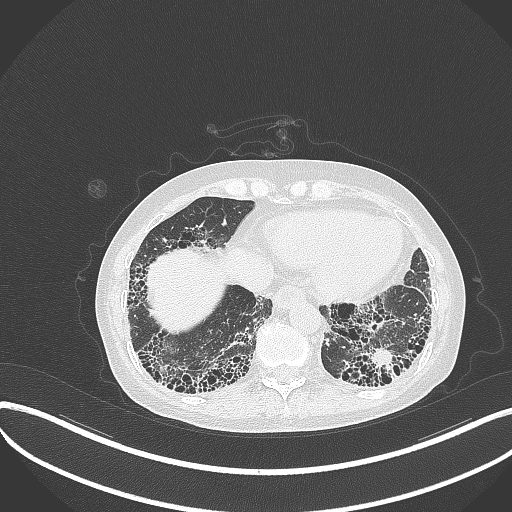
Chest CT, one axial slice; position 69 of 373 along the scan axis; 120 kVp; lung window (W 1500 / L -600 HU); 1 mm slice thickness; 512 × 512 image matrix. Patient: female, 56 years. Case-level facts recorded for this patient, not image findings: clinical TNM (as recorded): T1 N0 M0.
Annotated regions visible in this slice (rectangle marked by the reading radiologist):
- lung tumour (recorded histology: adenocarcinoma): box from (x=371, y=347) to (x=400, y=373) px